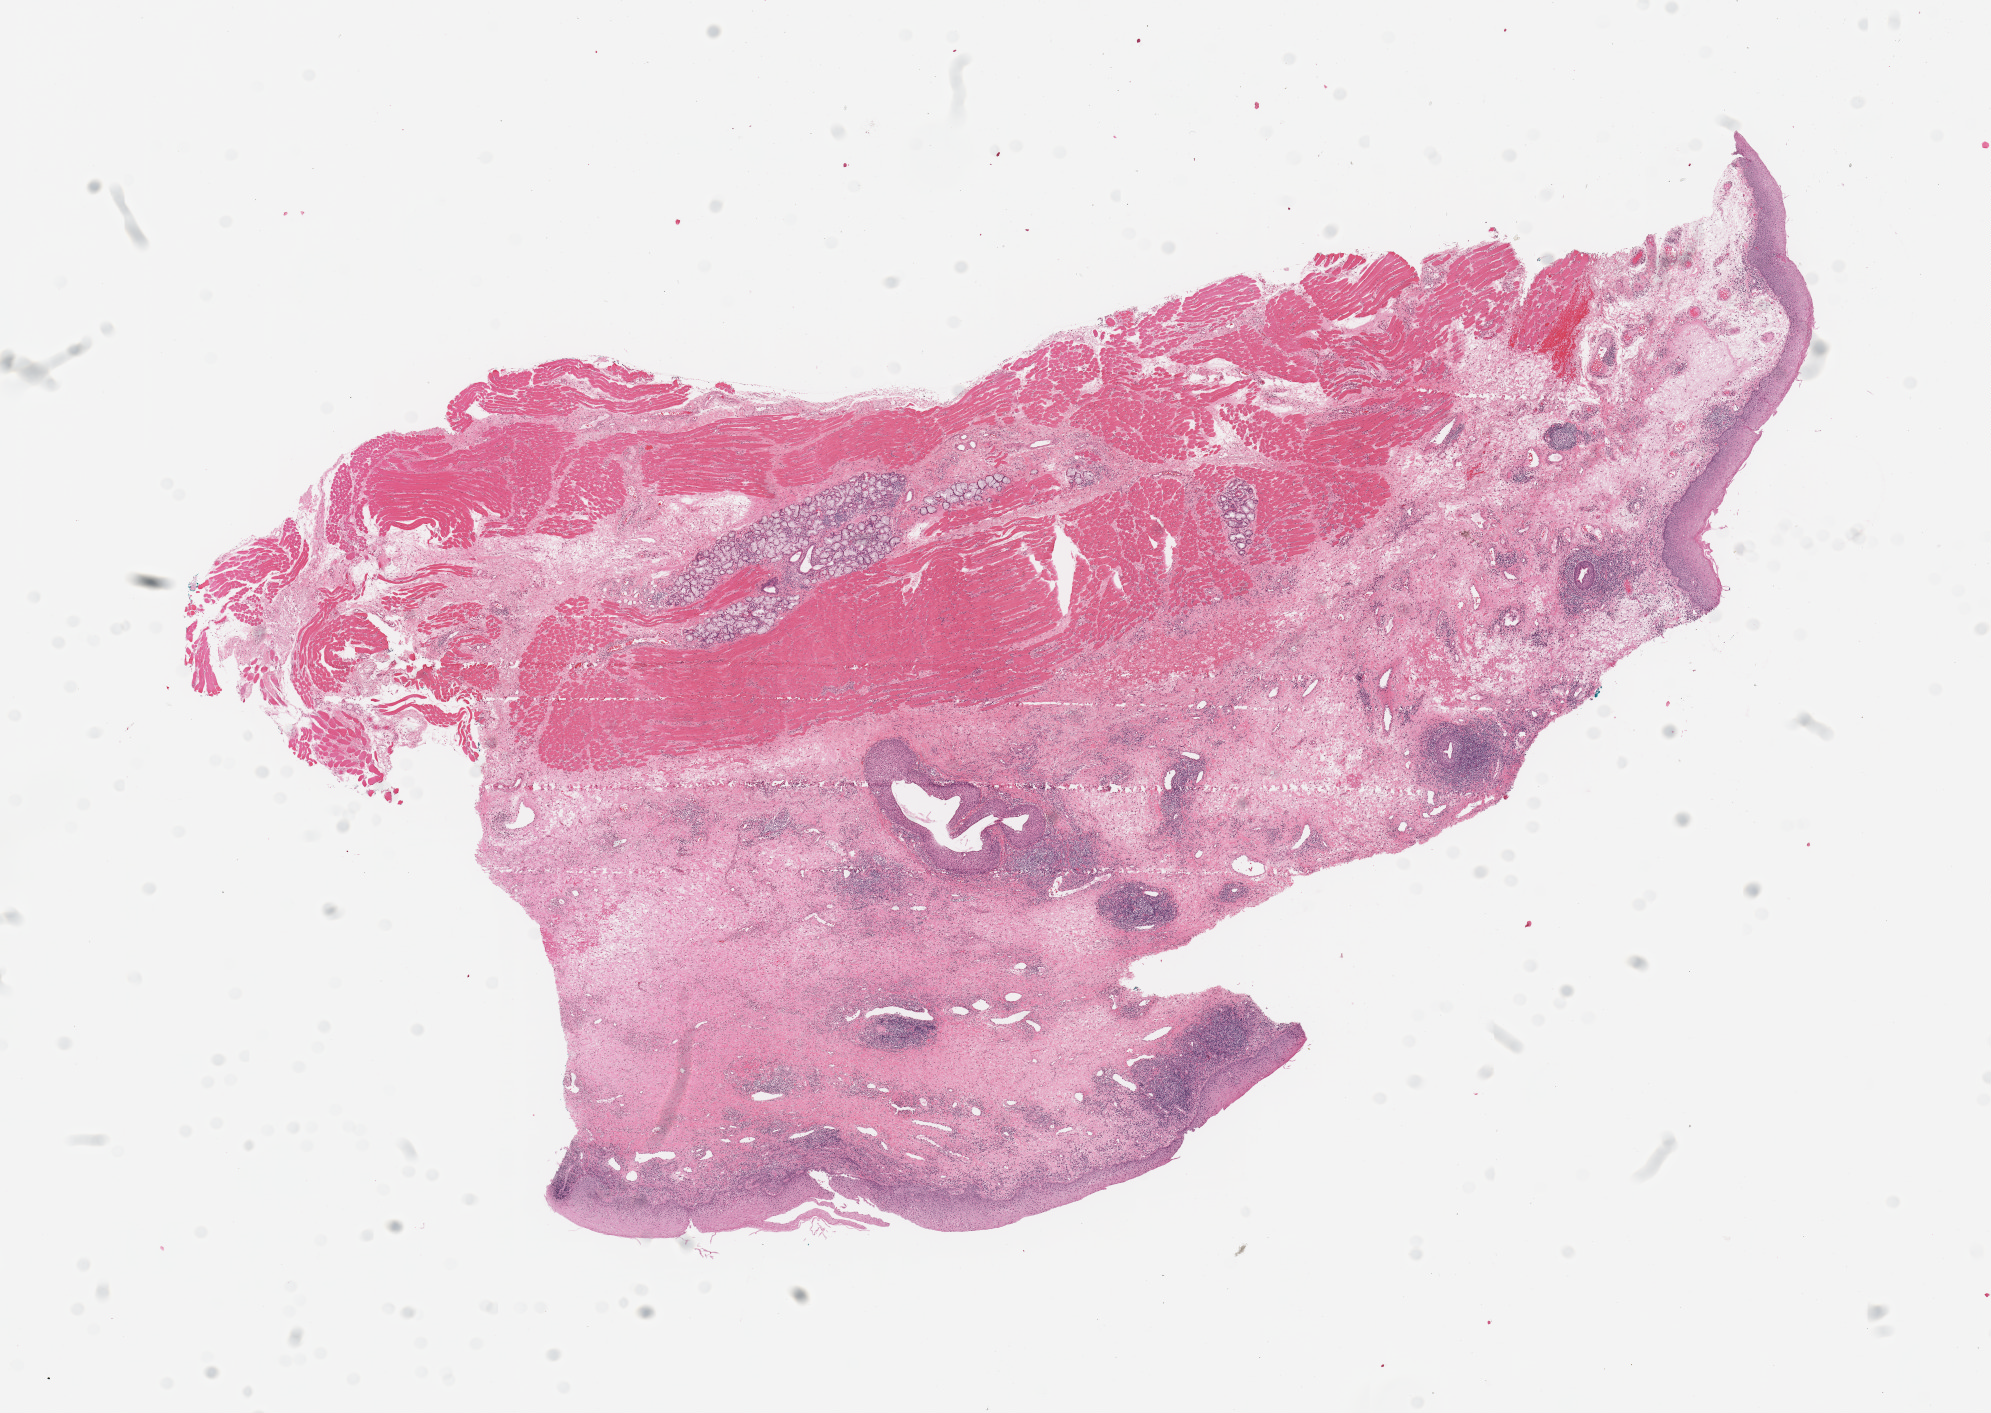
Hematoxylin and eosin (H&E) stained whole-slide image — shown as a low-resolution overview of the whole scanned area (about 15.8 x 11.2 mm, acquisition: 20x scan), normal (non-tumour) tissue sample, sampled site: larynx. 62-year-old male patient.
This section: normal (non-tumour) tissue from the same patient. Patient diagnosis: Squamous cell carcinoma, NOS (larynx, NOS).